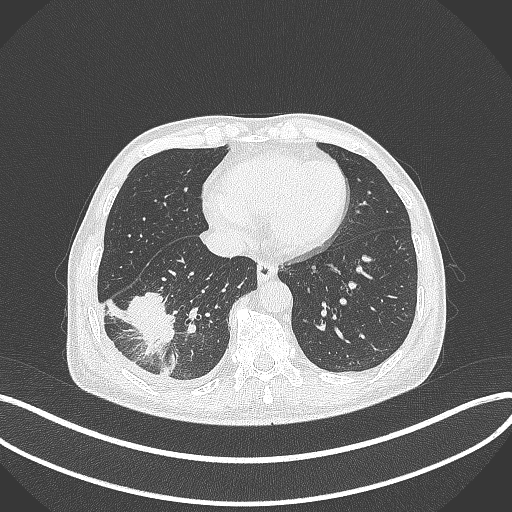
Chest CT, one axial slice. Position 116 of 388 along the scan axis. 120 kVp. Lung window (W 1500 / L -600 HU). 1 mm slice thickness. 512 × 512 image matrix, field of view 400 × 400 mm. Patient: male, 64 years. Case-level facts recorded for this patient, not image findings: clinical TNM (as recorded): T3 N0 M0; histopathological grade: G2-3.
Annotated regions visible in this slice (rectangle marked by the reading radiologist):
- lung tumour (recorded histology: adenocarcinoma): box from (x=124, y=286) to (x=176, y=359) px